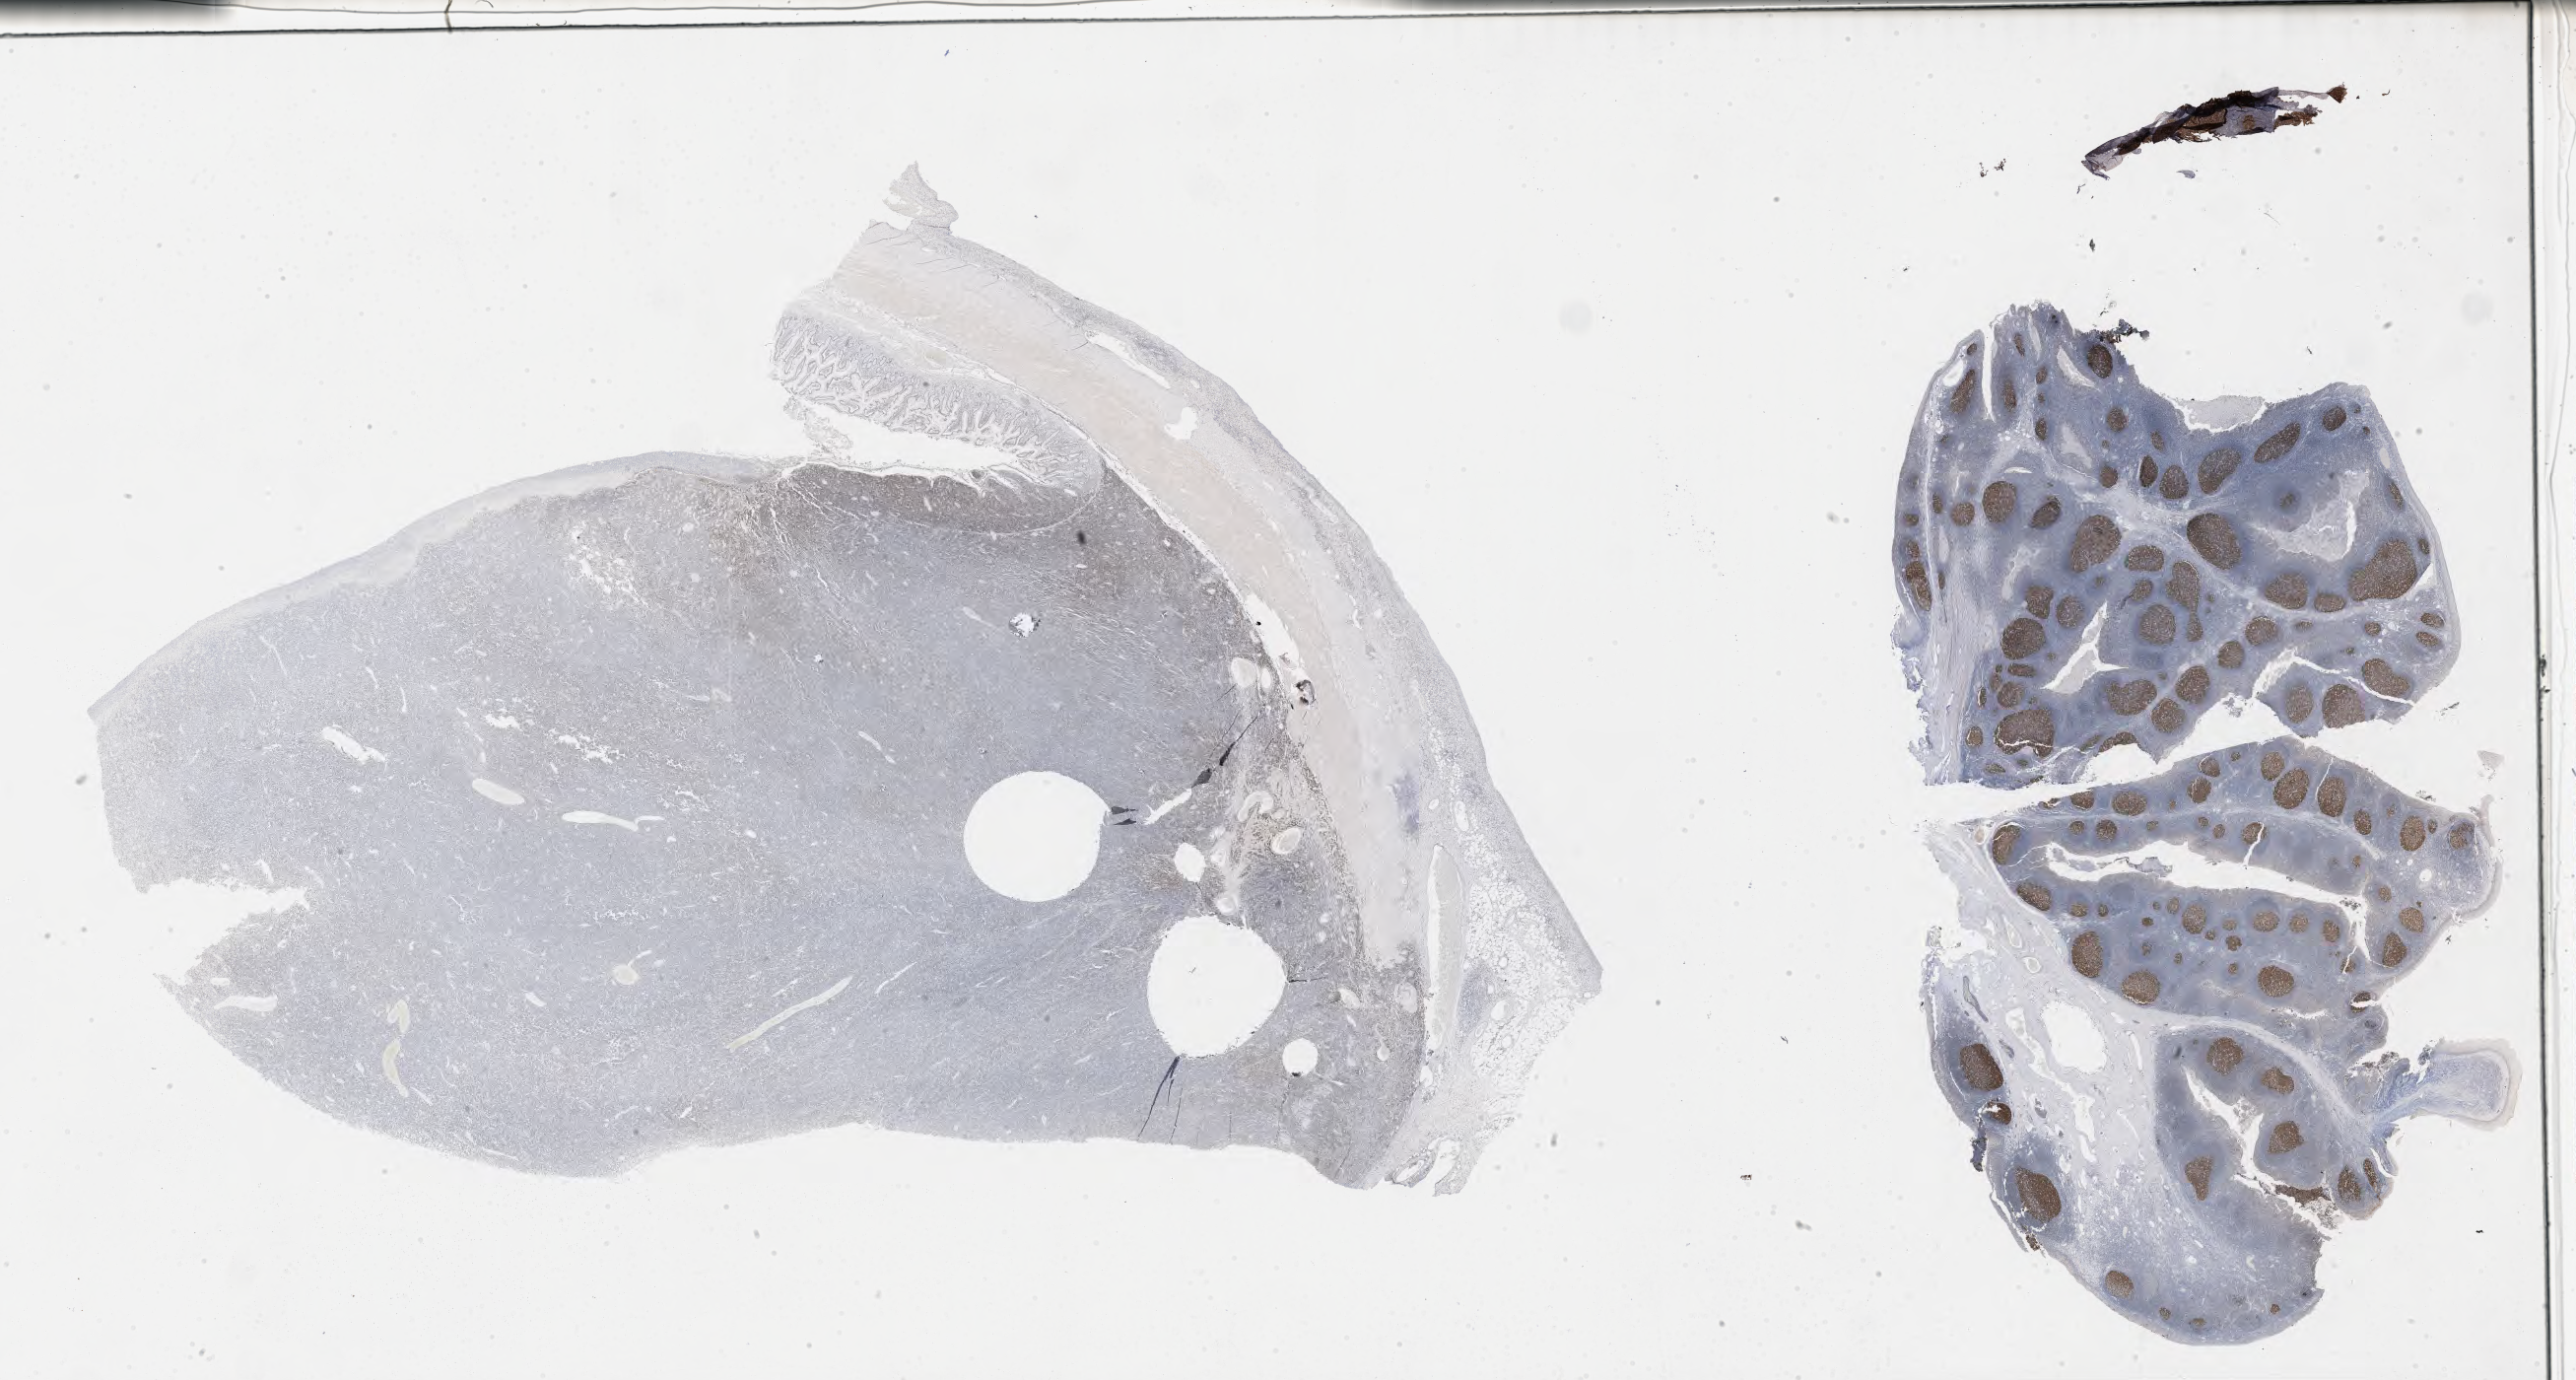
Whole-slide image, immunohistochemical stain for BCL6 — a low-resolution overview of the entire scanned area, about 42.3 x 22.6 mm; specimen: tumor tissue. Patient female; age 15 years.
* diagnosis: Burkitt lymphoma, NOS